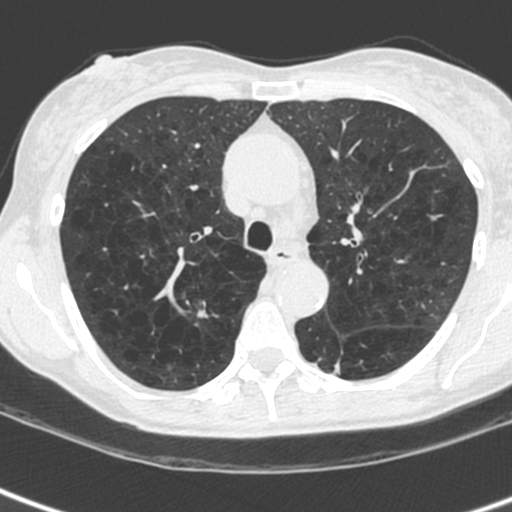
Low-dose screening chest CT, axial slice, first (baseline) screen, lung window (W 1500 / L -600 HU), 1.3 mm slice thickness, standard (soft-tissue) reconstruction kernel (C), 512 × 512 image matrix. Female, age 61 years at enrolment.
Expert reader's lesion annotation, bounding box <176,293,227,341> (left, top, right, bottom; pixels). No non-calcified nodule or mass ≥4 mm was recorded by the screening reader at this exam. Official screen result: negative screen, no significant abnormalities. Participant outcome: lung cancer diagnosed 836 days after this screen (after the third annual screen) — non-small cell carcinoma, right upper lobe, undifferentiated (G4), stage IA (AJCC 6th edition), 15 mm at pathology.